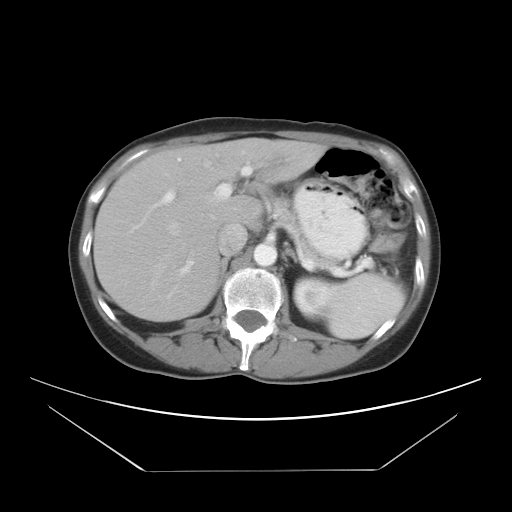
Contrast-enhanced abdominal CT, one axial slice. Position 18 of 30 along the scan axis. Reconstruction kernel STANDARD. Intravenous contrast given. Soft-tissue window (W 400 / L 40 HU). 7.5 mm slice thickness. 512 × 512 image matrix, field of view 412 × 412 mm. Female patient, age 54 years. Case-level facts recorded for this patient, not image findings: diagnosis: colorectal cancer liver metastases, imaged before liver resection; multiple liver metastases: yes; largest metastasis: 2.5 cm.
Structures marked on this image (manually delineated by an expert):
- hepatic veins: bounding box [x1, y1, x2, y2] px = [151, 224, 184, 300]
- liver: [95, 140, 324, 322]
- planned liver remnant (the part of the liver to remain after resection): [95, 142, 258, 322]
- portal vein (with intrahepatic branches): [129, 156, 251, 273]
- liver metastasis: [277, 161, 286, 169]